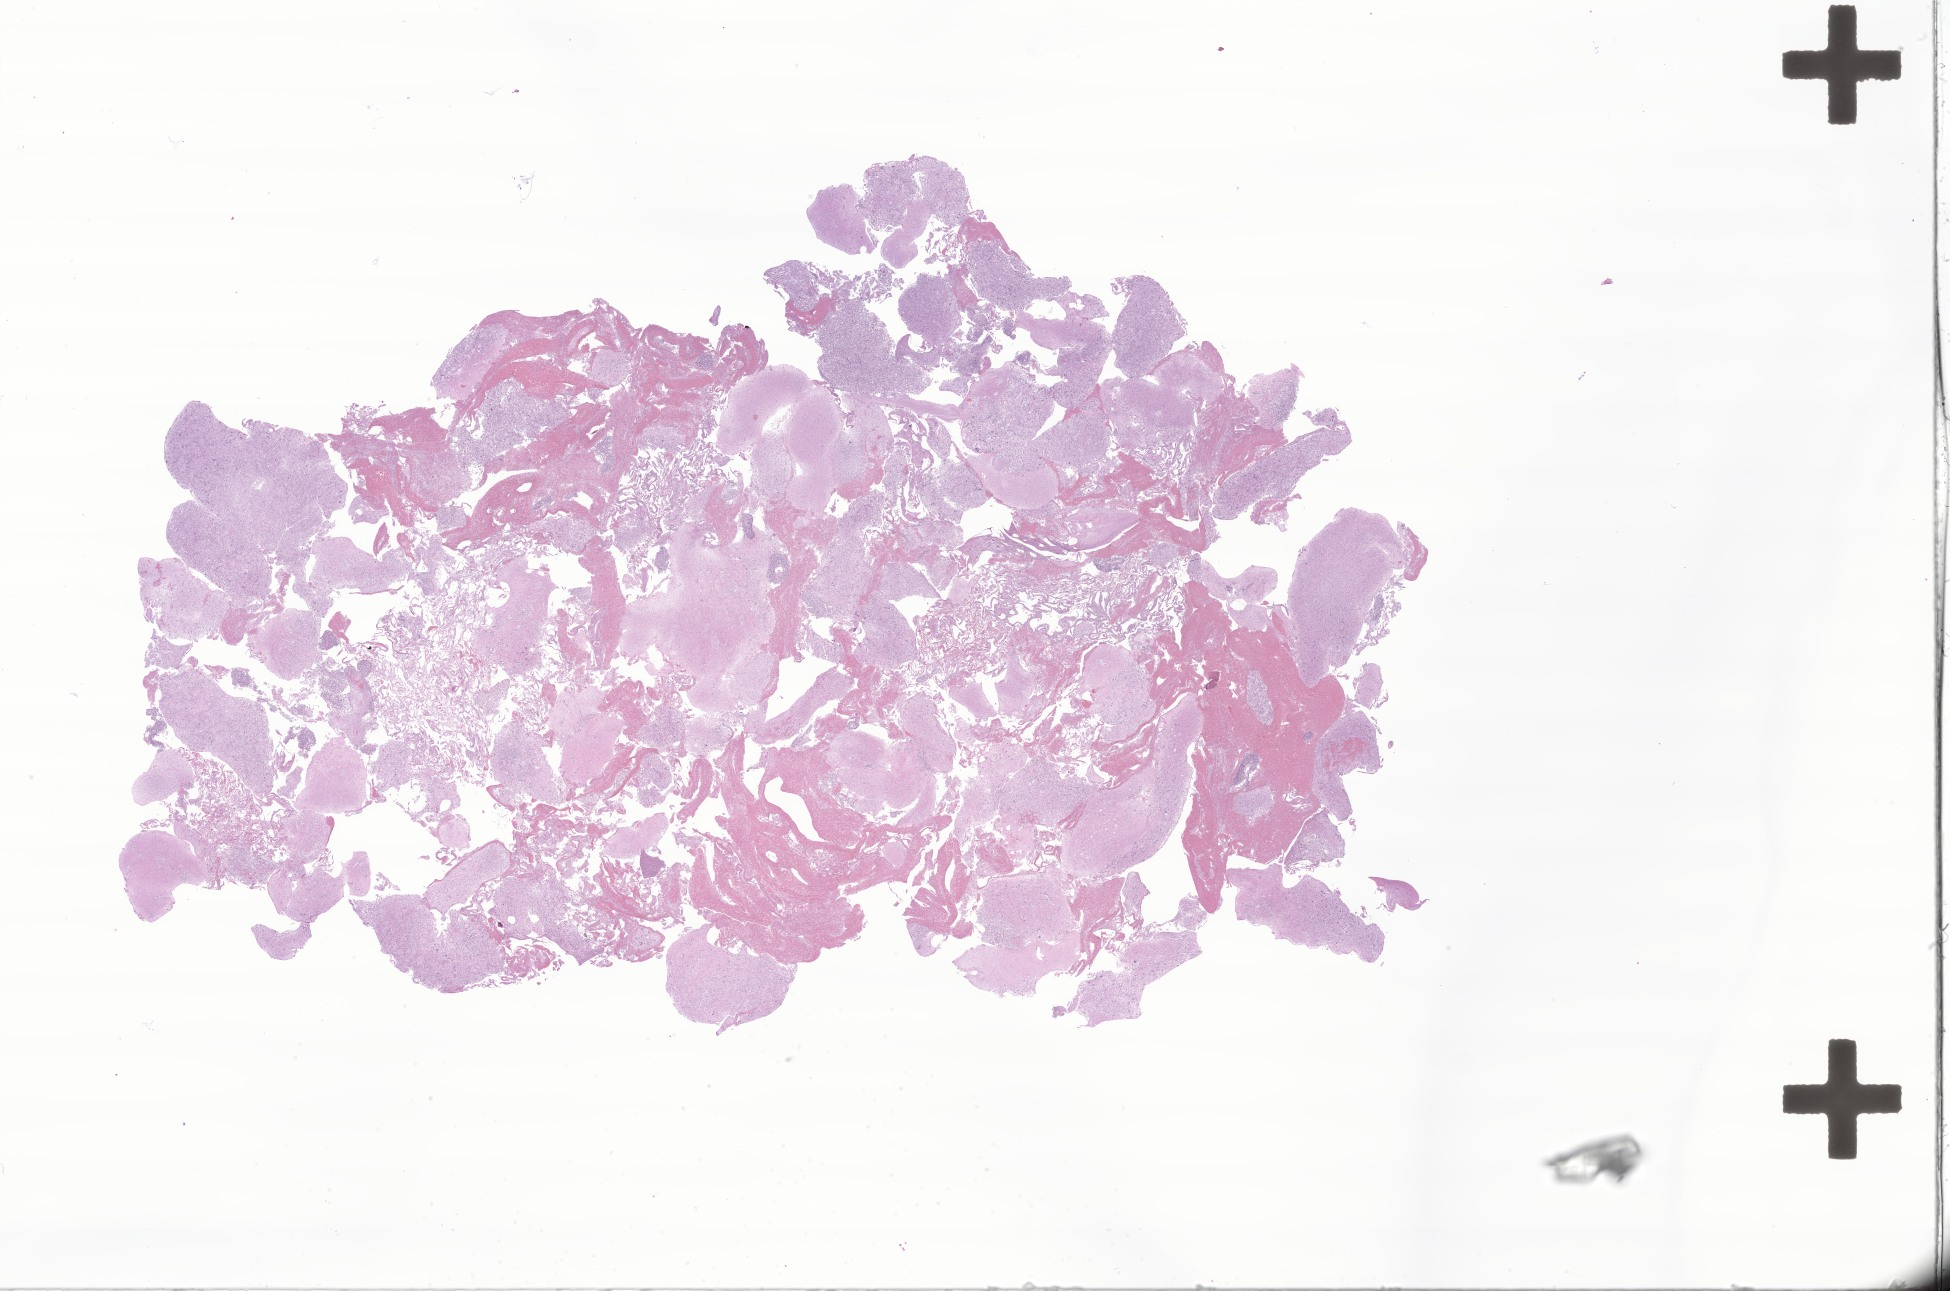
H&E whole-slide image of tumor tissue from the brain — low-resolution overview of the scanned area, about 32.9 x 21.8 mm. FFPE section. Female patient, age 205 months (17 years 1 month).
• diagnosis: Glioma, malignant